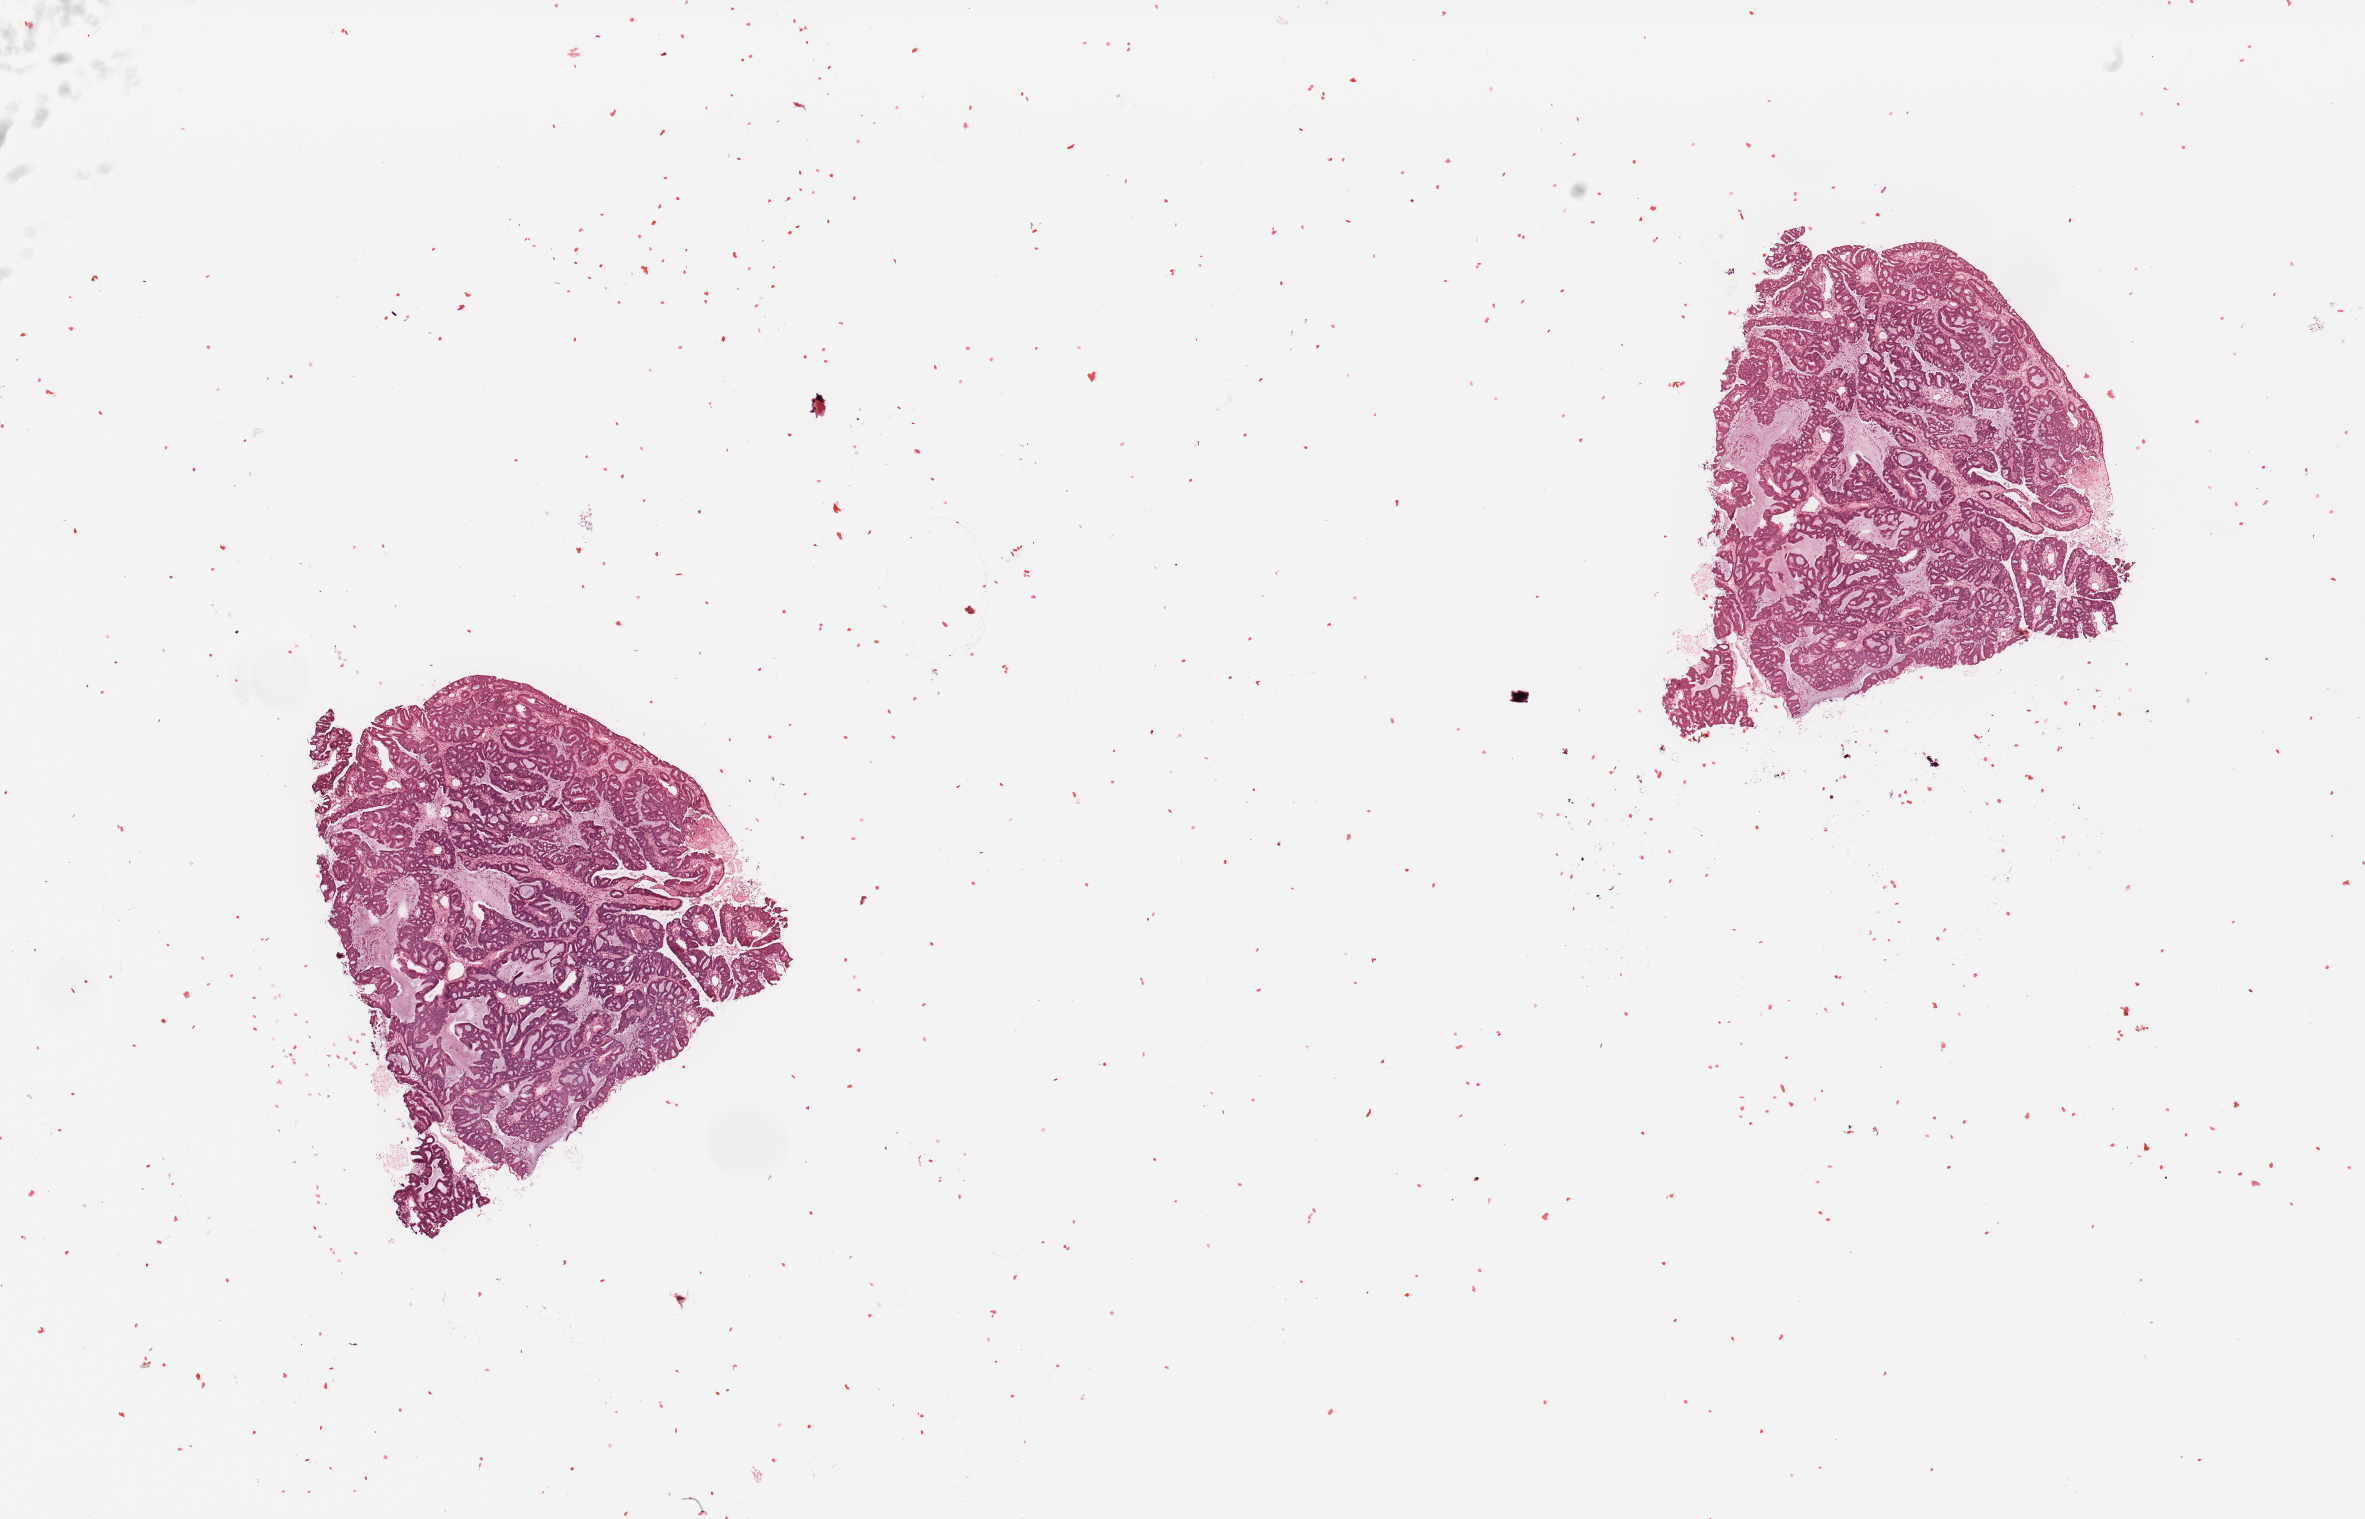
Whole-slide histology image, Hematoxylin and eosin (H&E) stained — low-resolution overview of the scanned area, about 18.7 x 12.0 mm (acquisition: 20x scan); tumour tissue sample, sampled site: uterus. Patient: female, age 80 years. Histologic grade: G2 (moderately differentiated). Pathologist review of this section (percent, as recorded): tumour nuclei 90%, necrosis 2%.
- primary tumour site (as recorded): posterior endometrium
- diagnosis: Endometrioid adenocarcinoma, NOS
- AJCC pathologic stage: I